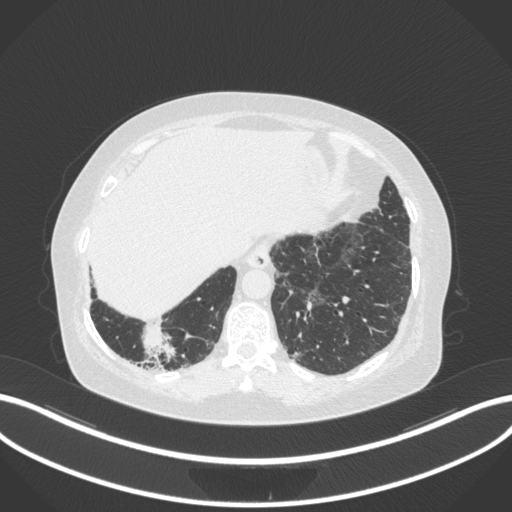
Chest CT, one axial slice; slice 24 of 303 in the series (ordered by position); lung window (W 1500 / L -600 HU); 1 mm slice thickness; 512 × 512 image matrix, field of view 400 × 400 mm. Patient: female, 65 years. Case-level facts recorded for this patient, not image findings: clinical TNM (as recorded): T2b N1 M0; histopathological grade: G1.
Outlined on this slice (bounding box drawn by a radiologist):
- lung tumour (recorded histology: adenocarcinoma): bounding box [x1, y1, x2, y2] px = [136, 324, 183, 363]